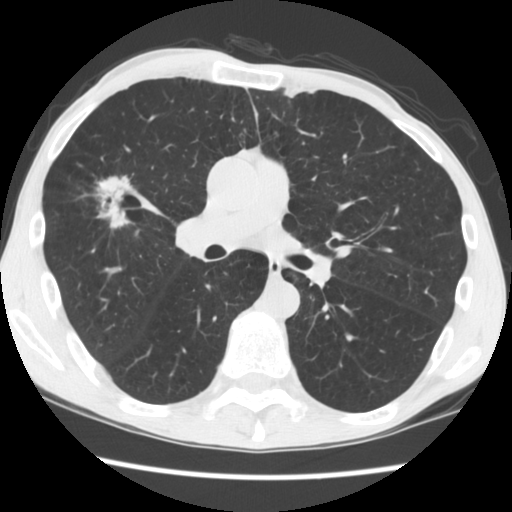
Chest CT (low-dose screening protocol), one axial image; second screening round (one year after baseline); lung window (W 1500 / L -600 HU); 2.5 mm slice thickness; 120 kVp; slice 84 of 181 in the series. Male participant, aged 56 years at enrolment.
Lesion marked by an expert reader, box from (x=85, y=162) to (x=147, y=231) px. The screening reader recorded 2 non-calcified nodules or masses ≥4 mm on this exam (right upper lobe, left upper lobe); which of them this box marks is not recorded. Participant outcome: lung cancer diagnosed 101 days after this screen — squamous cell carcinoma, NOS, right upper lobe, right middle lobe, well differentiated (G1), stage IA (AJCC 6th edition), 27 mm at pathology.